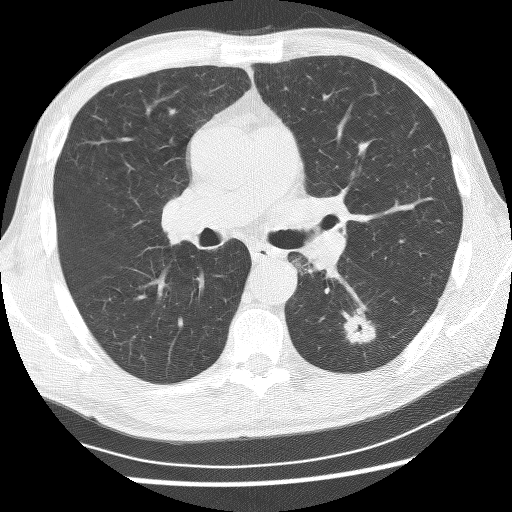
Low-dose screening chest CT, one axial slice; slice 146 of 253 in the series (ordered by position); 120 kVp; lung window (W 1500 / L -600 HU); 512 × 512 image matrix, field of view 340 × 340 mm.
Structures marked on this image (expert manual segmentation):
- lesion 1 (tumor, lower lobe of left lung): box from (x=342, y=308) to (x=376, y=344) px